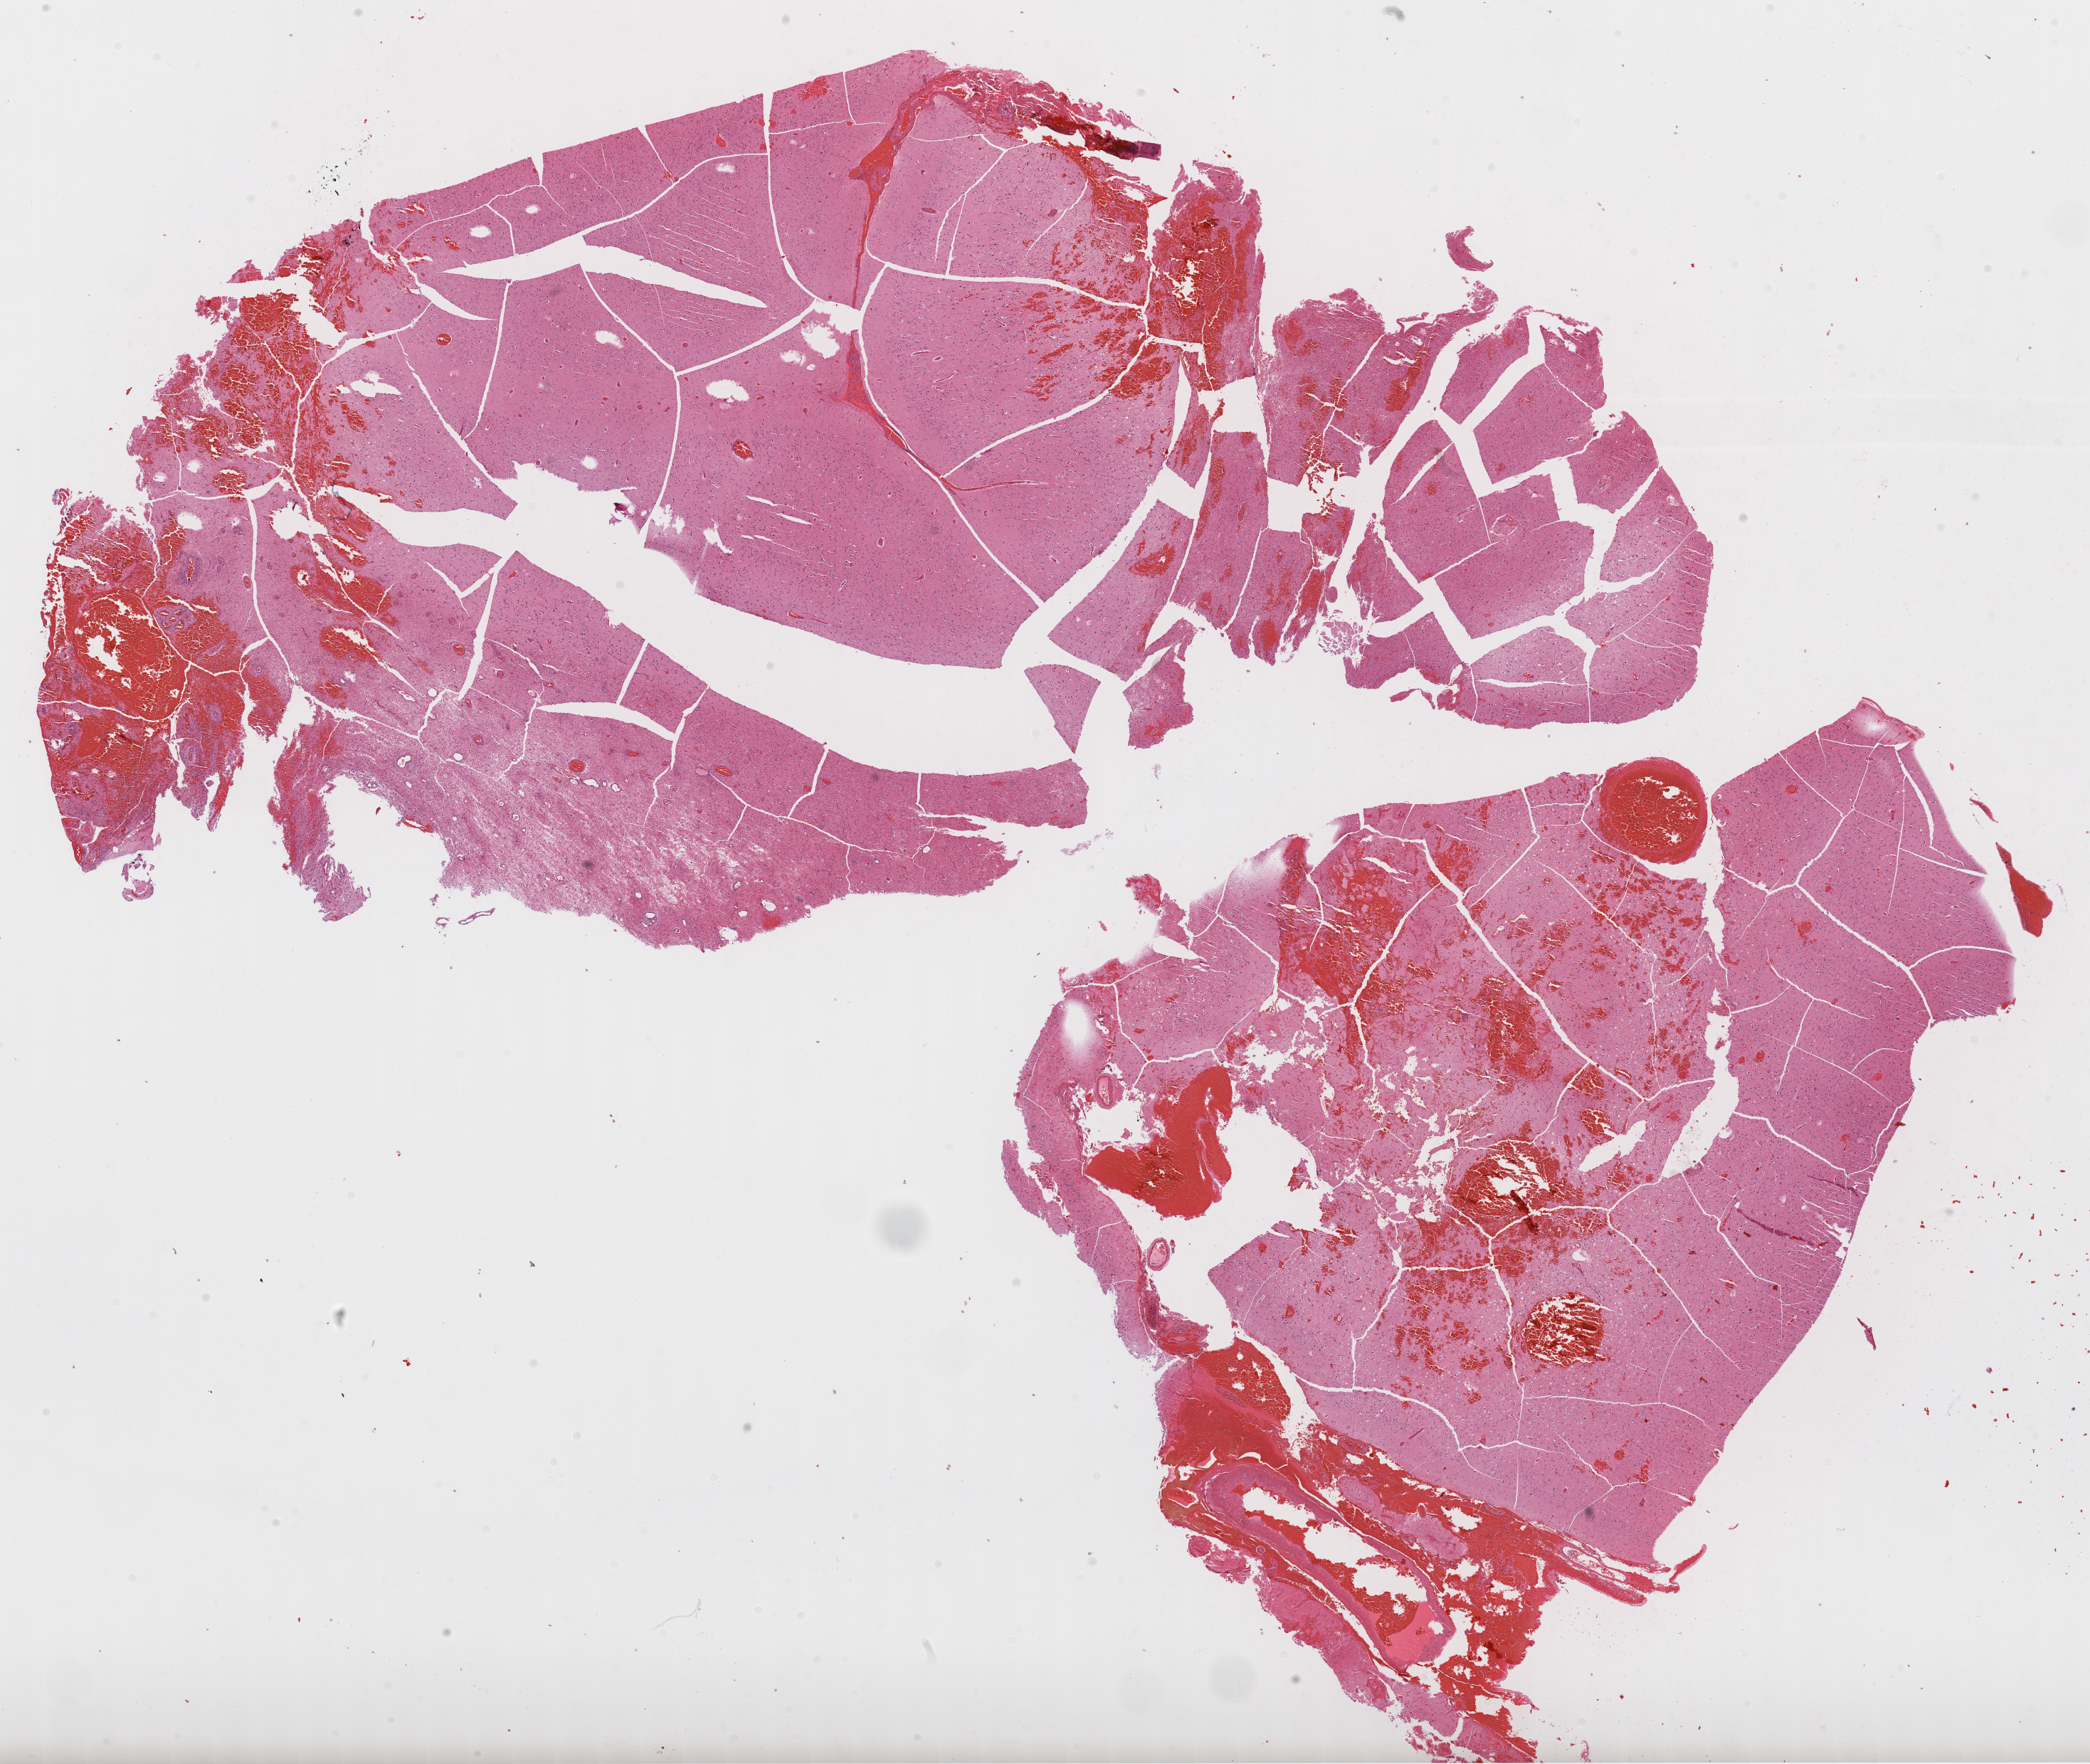
H&E-stained whole-slide image, a low-resolution overview of the entire scanned area, about 23.7 x 20.0 mm (from a 20x scan); FFPE section; primary tumour sample from the brain. Male patient; age at initial diagnosis 67 years.
Diagnosis: Glioblastoma.